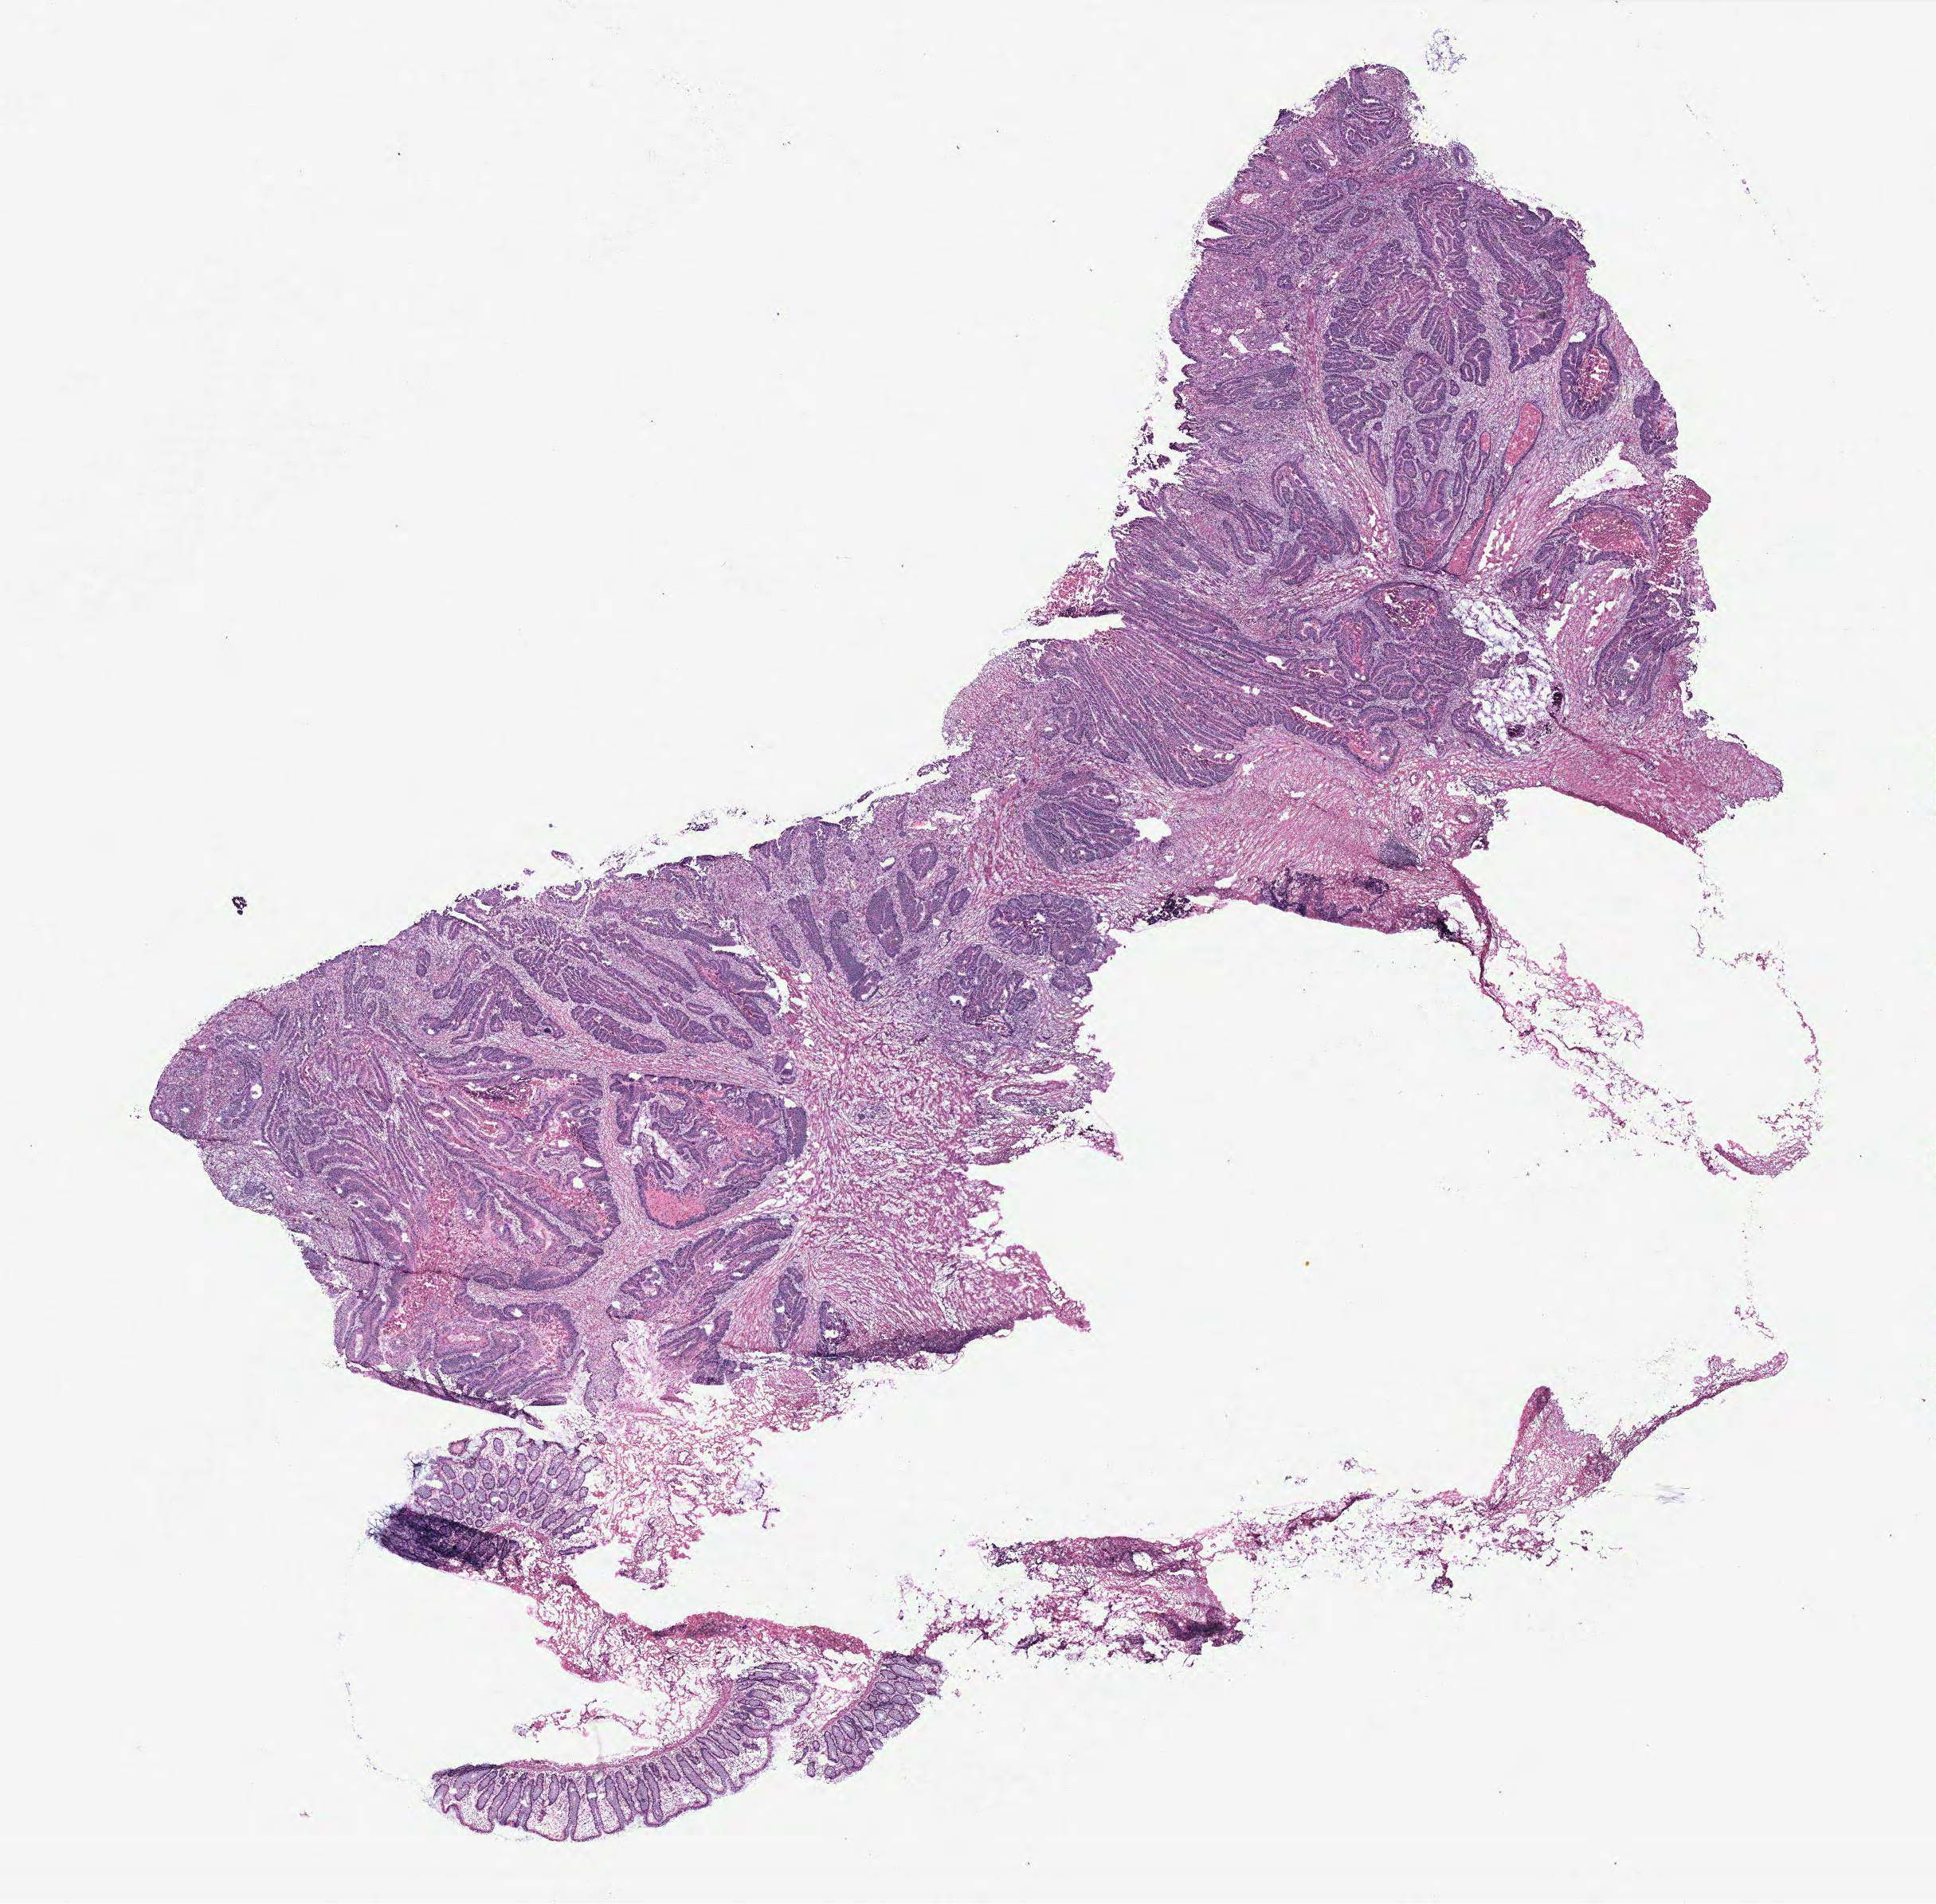
H&E-stained whole-slide image — shown as a low-resolution overview of the whole scanned area (about 19.4 x 19.1 mm, acquisition: 40x scan). Tumour tissue sample, colon. Female, 56 y/o.
* diagnosis: Adenocarcinoma, NOS
* primary tumour site (as recorded): colon
* AJCC pathologic stage: IIA